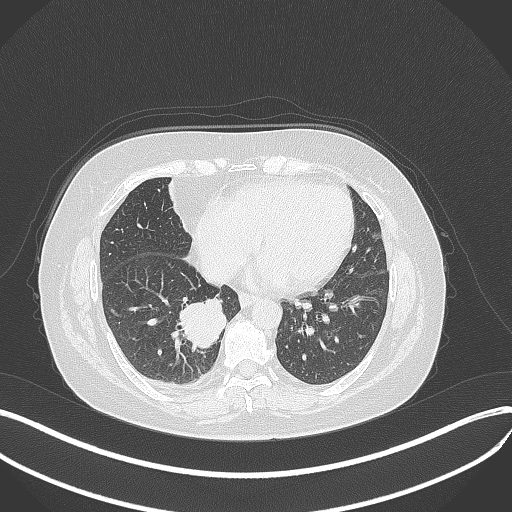
Chest CT, one axial slice. Position 129 of 381 along the scan axis. 120 kVp. Lung window (W 1500 / L -600 HU). 1 mm slice thickness. 512 × 512 image matrix, field of view 400 × 400 mm. Patient: female, 56 years. From the clinical record (not read from this slice): clinical TNM (as recorded): T2b N1 M0.
Outlined on this slice (bounding box drawn by a radiologist):
- lung tumour (recorded histology: small cell carcinoma): bounding box (x1, y1, x2, y2) in pixels: (177, 294, 230, 353)